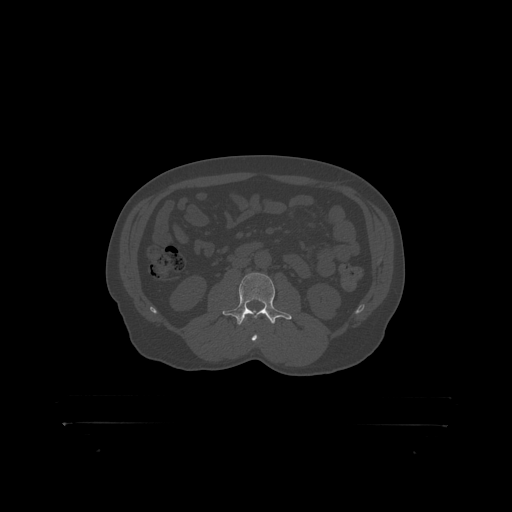
CT including the spine, one axial slice. Position 271 of 399 along the scan axis. Reconstruction kernel STANDARD. 120 kVp. Bone window (W 1800 / L 400 HU). 1.25 mm slice thickness. 512 × 512 image matrix, field of view 650 × 650 mm. Male patient, age 46 years. Case-level facts recorded for this patient, not image findings: primary cancer: skin.
Annotated regions visible in this slice (semi-automatic segmentation, software-assisted and operator-edited):
- L3 vertebra: bounding box <228,273,282,319> (left, top, right, bottom; pixels)